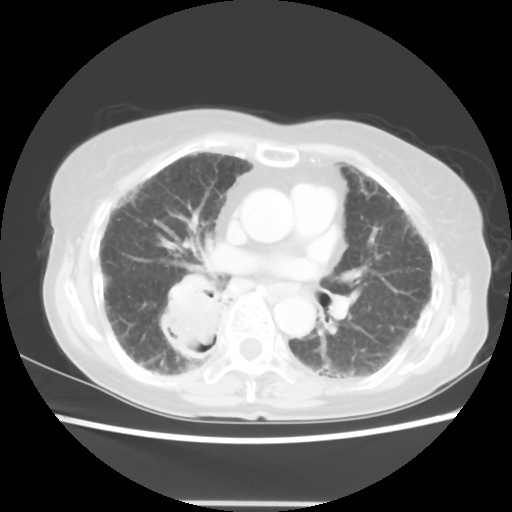
Chest CT, one axial slice. Reconstruction kernel STANDARD. Lung window (W 1500 / L -600 HU). 5 mm slice thickness. 512 × 512 image matrix. Patient: female, 71 years. Case-level facts recorded for this patient, not image findings: clinical TNM (as recorded): T3 N0 M0.
Annotated regions visible in this slice (rectangle marked by the reading radiologist):
- lung tumour (recorded histology: squamous cell carcinoma): bounding box [x1, y1, x2, y2] px = [156, 286, 232, 362]